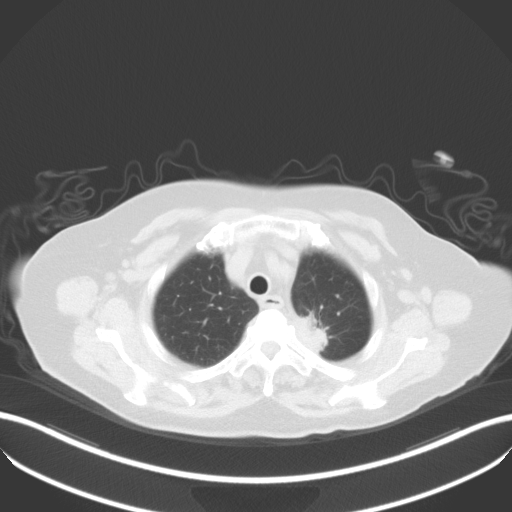
Chest CT, one axial slice. Position 34 of 42 along the scan axis. Reconstruction kernel B31f. Lung window (W 1500 / L -600 HU). 6 mm slice thickness. 512 × 512 image matrix, field of view 400 × 400 mm. Patient: female, 81 years. From the clinical record (not read from this slice): clinical TNM (as recorded): T2a N0 M0.
Structures marked on this image (rectangle marked by the reading radiologist):
- lung tumour (recorded histology: adenocarcinoma): bounding box (x1, y1, x2, y2) in pixels: (286, 303, 336, 356)